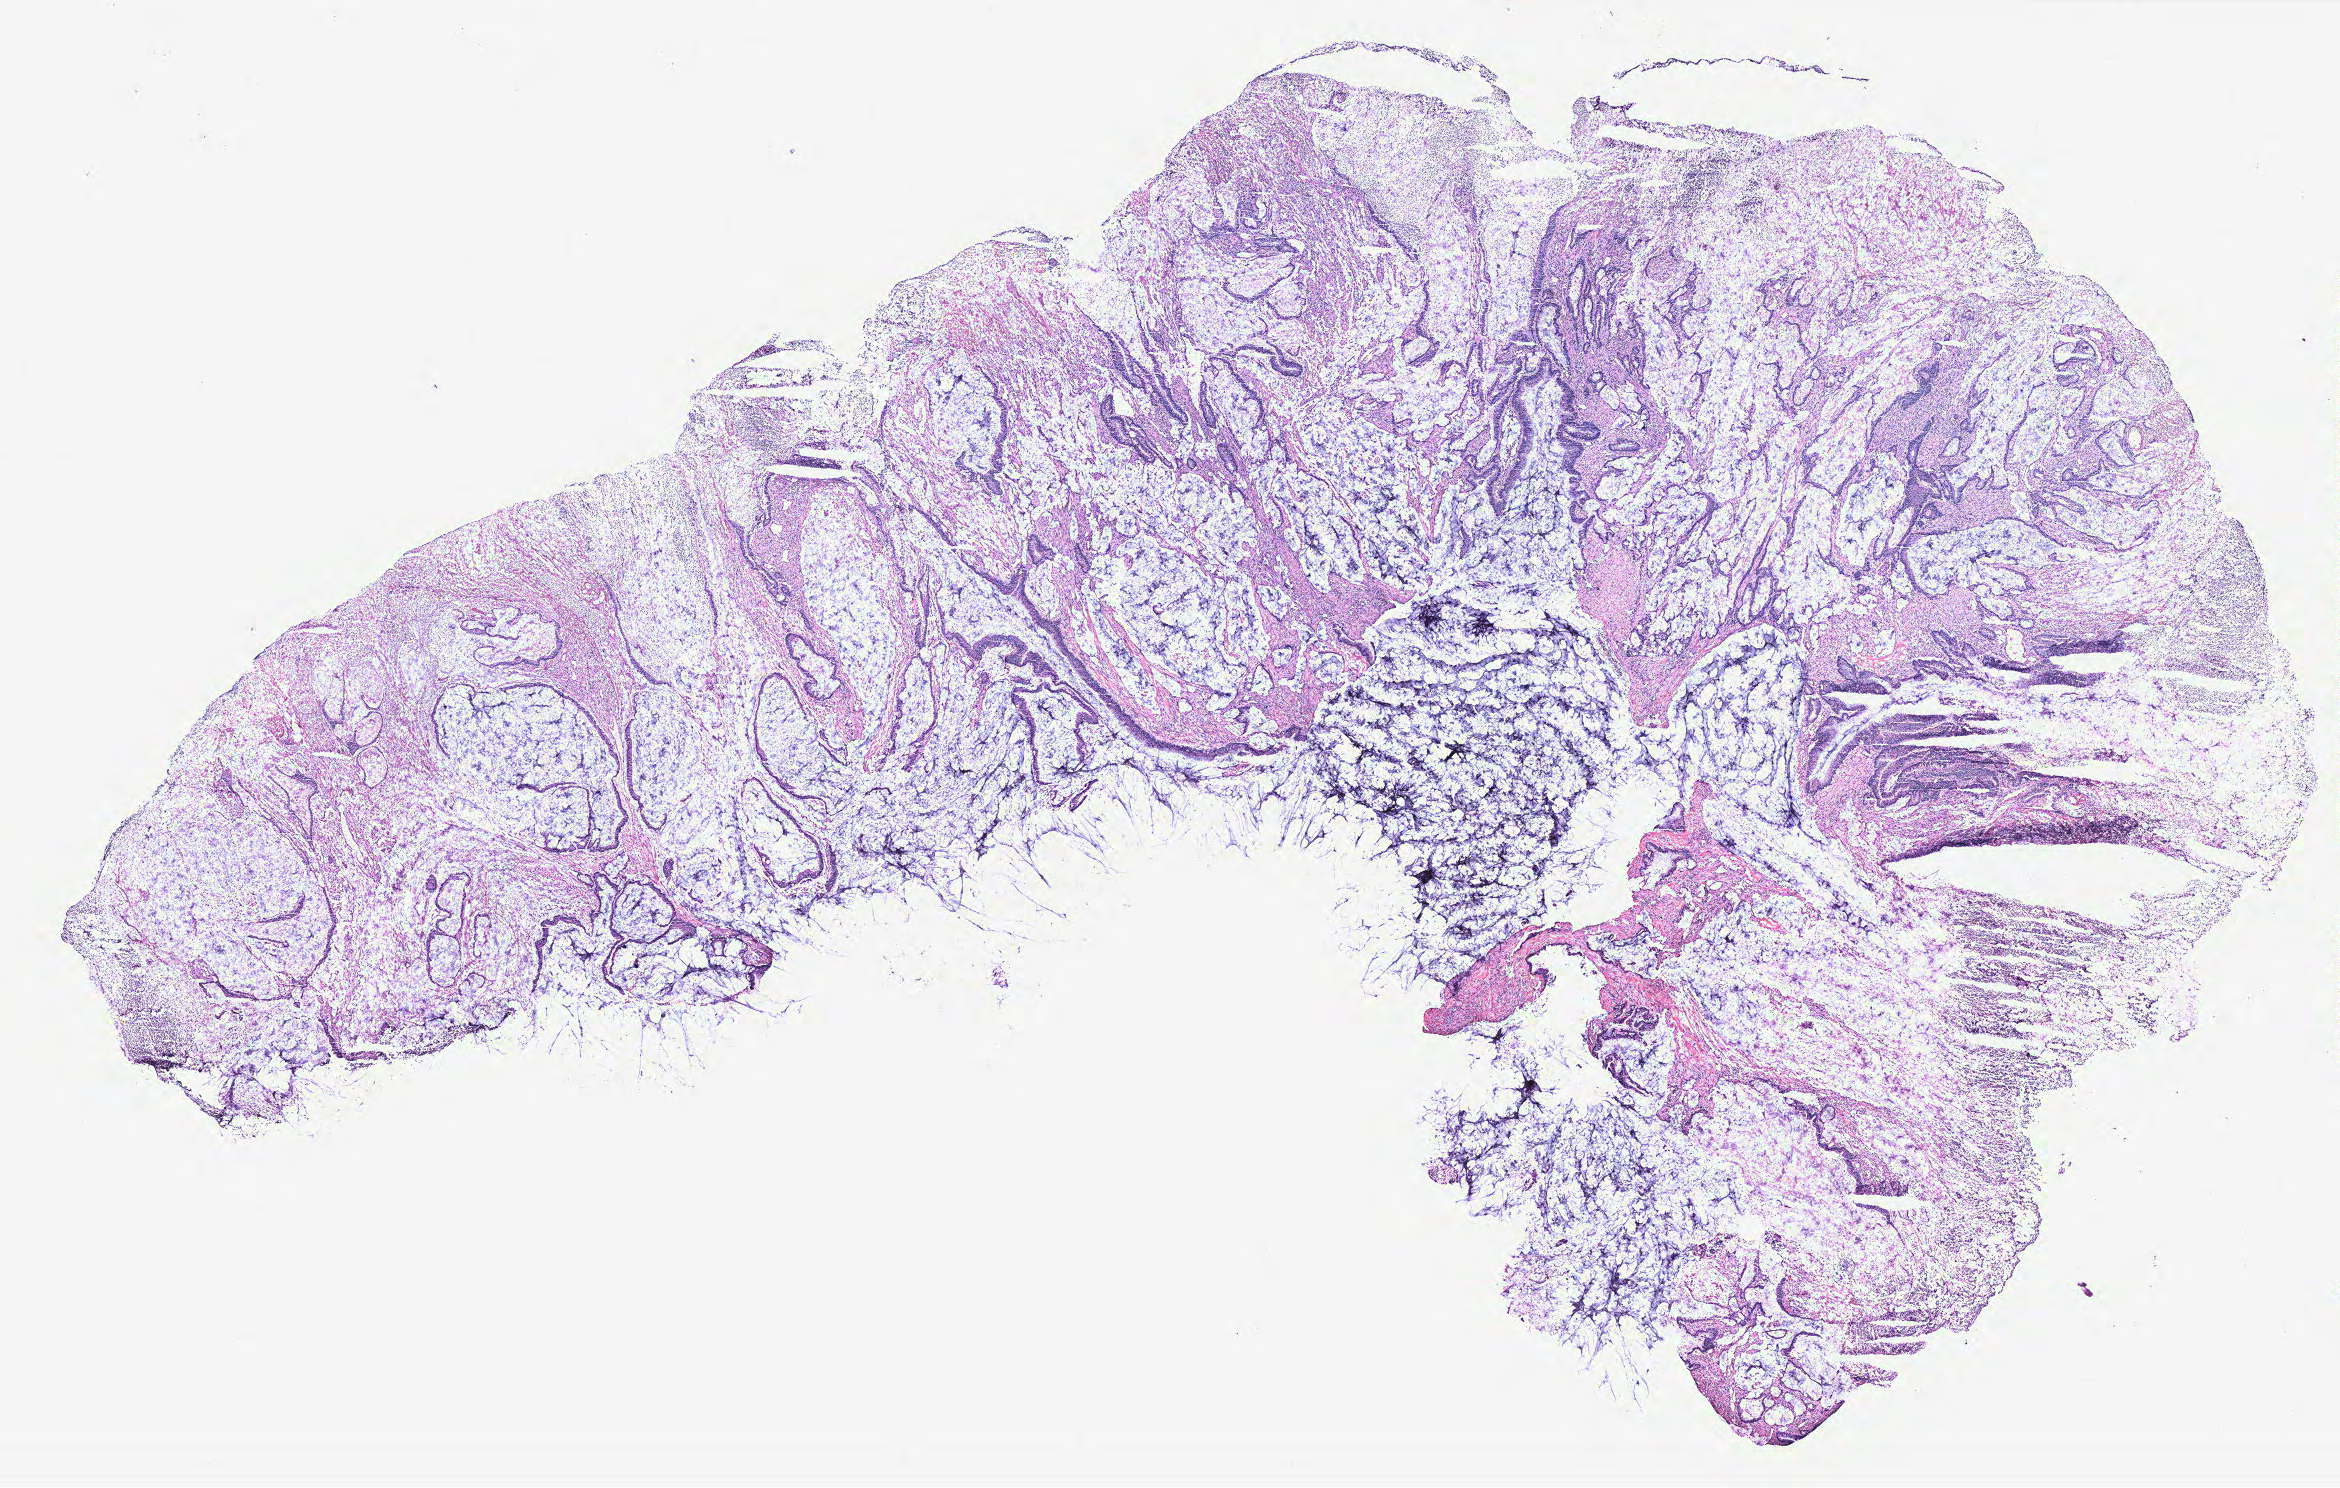
H&E whole-slide image — low-resolution overview of the scanned area, about 18.7 x 11.9 mm; colon, tissue type not recorded.
- patient diagnosis (cohort enrolment): colon cancer (colon)